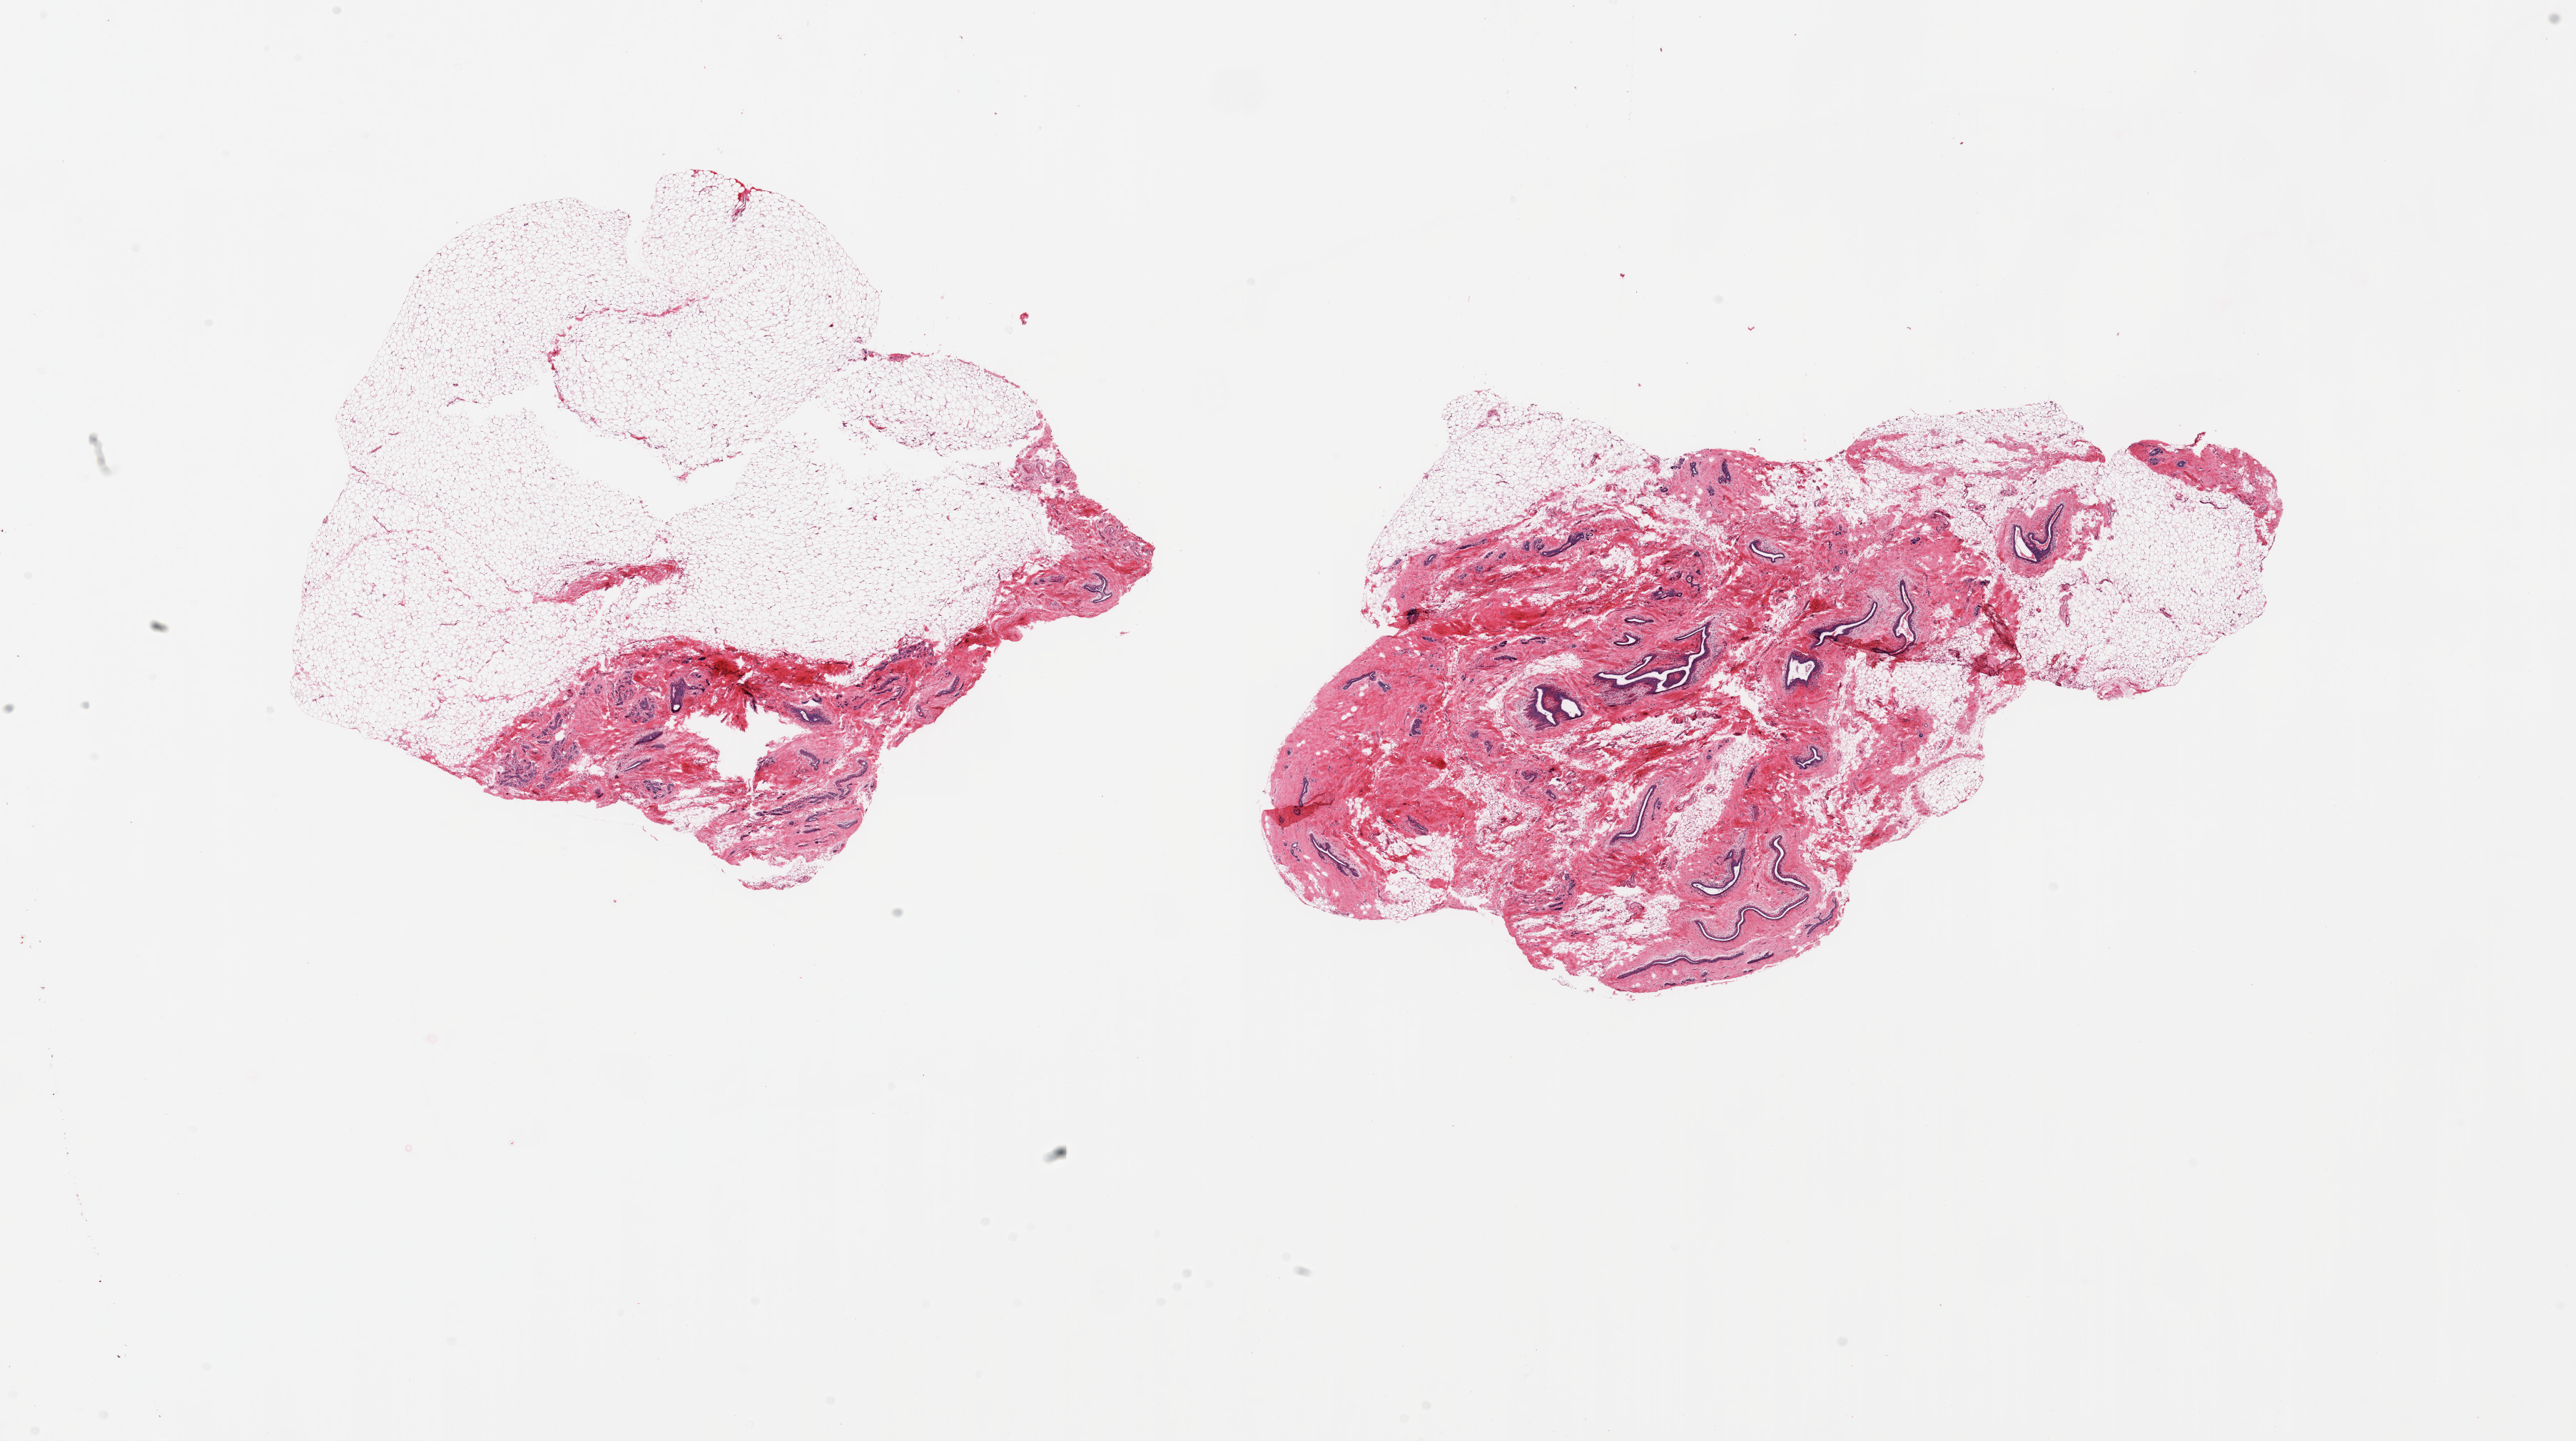
Haematoxylin and eosin whole-slide image — a low-resolution overview of the entire scanned area, about 28.5 x 16.0 mm (slide scanned at 20x), PAXgene-fixed, paraffin-embedded tissue, sampled site (target tissue): breast, donor tissue sample.
Review note (as recorded): 2 pieces;; ducts & atrophic lobules; 1 piece has 30% fat content, other has 70% fat content.